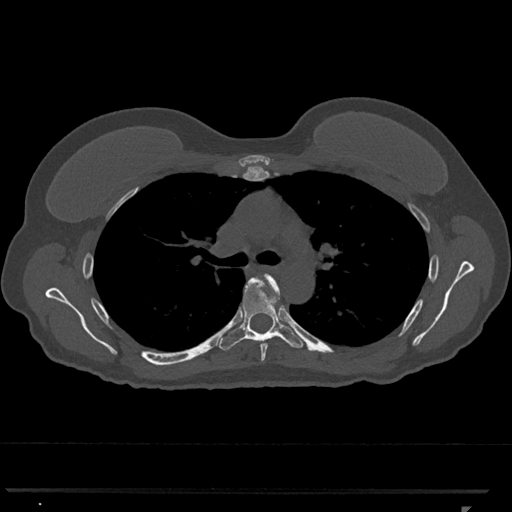
CT including the spine, one axial slice. Slice 777 of 793 in the series (ordered by position). 120 kVp. Bone window (W 1800 / L 400 HU). 512 × 512 image matrix. Female patient, age 62 years. Case-level facts recorded for this patient, not image findings: primary cancer: renal.
Structures marked on this image (semi-automatic segmentation, software-assisted and operator-edited):
- T5 vertebra: bounding box (x1, y1, x2, y2) in pixels: (260, 274, 280, 362)
- T6 vertebra: (219, 277, 304, 351)